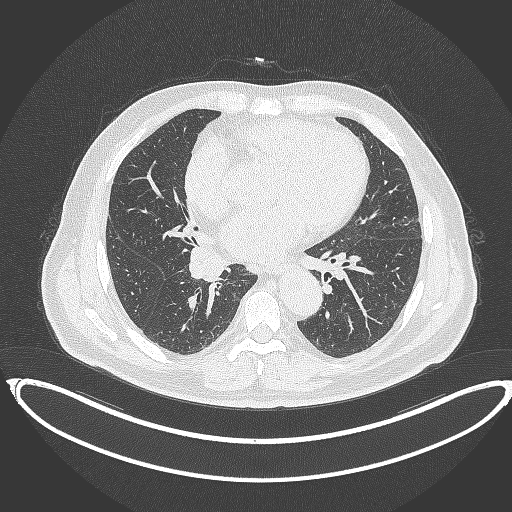
Chest CT, one axial slice. Slice 190 of 387 in the series (ordered by position). Reconstruction kernel B70f. 120 kVp. Lung window (W 1500 / L -600 HU). 1 mm slice thickness. 512 × 512 image matrix, field of view 448 × 448 mm. Patient: male, 61 years. Case-level facts recorded for this patient, not image findings: clinical TNM (as recorded): T1b N1 M0.
Structures marked on this image (rectangle marked by the reading radiologist):
- lung tumour (recorded histology: squamous cell carcinoma): bounding box <185,243,233,283> (left, top, right, bottom; pixels)